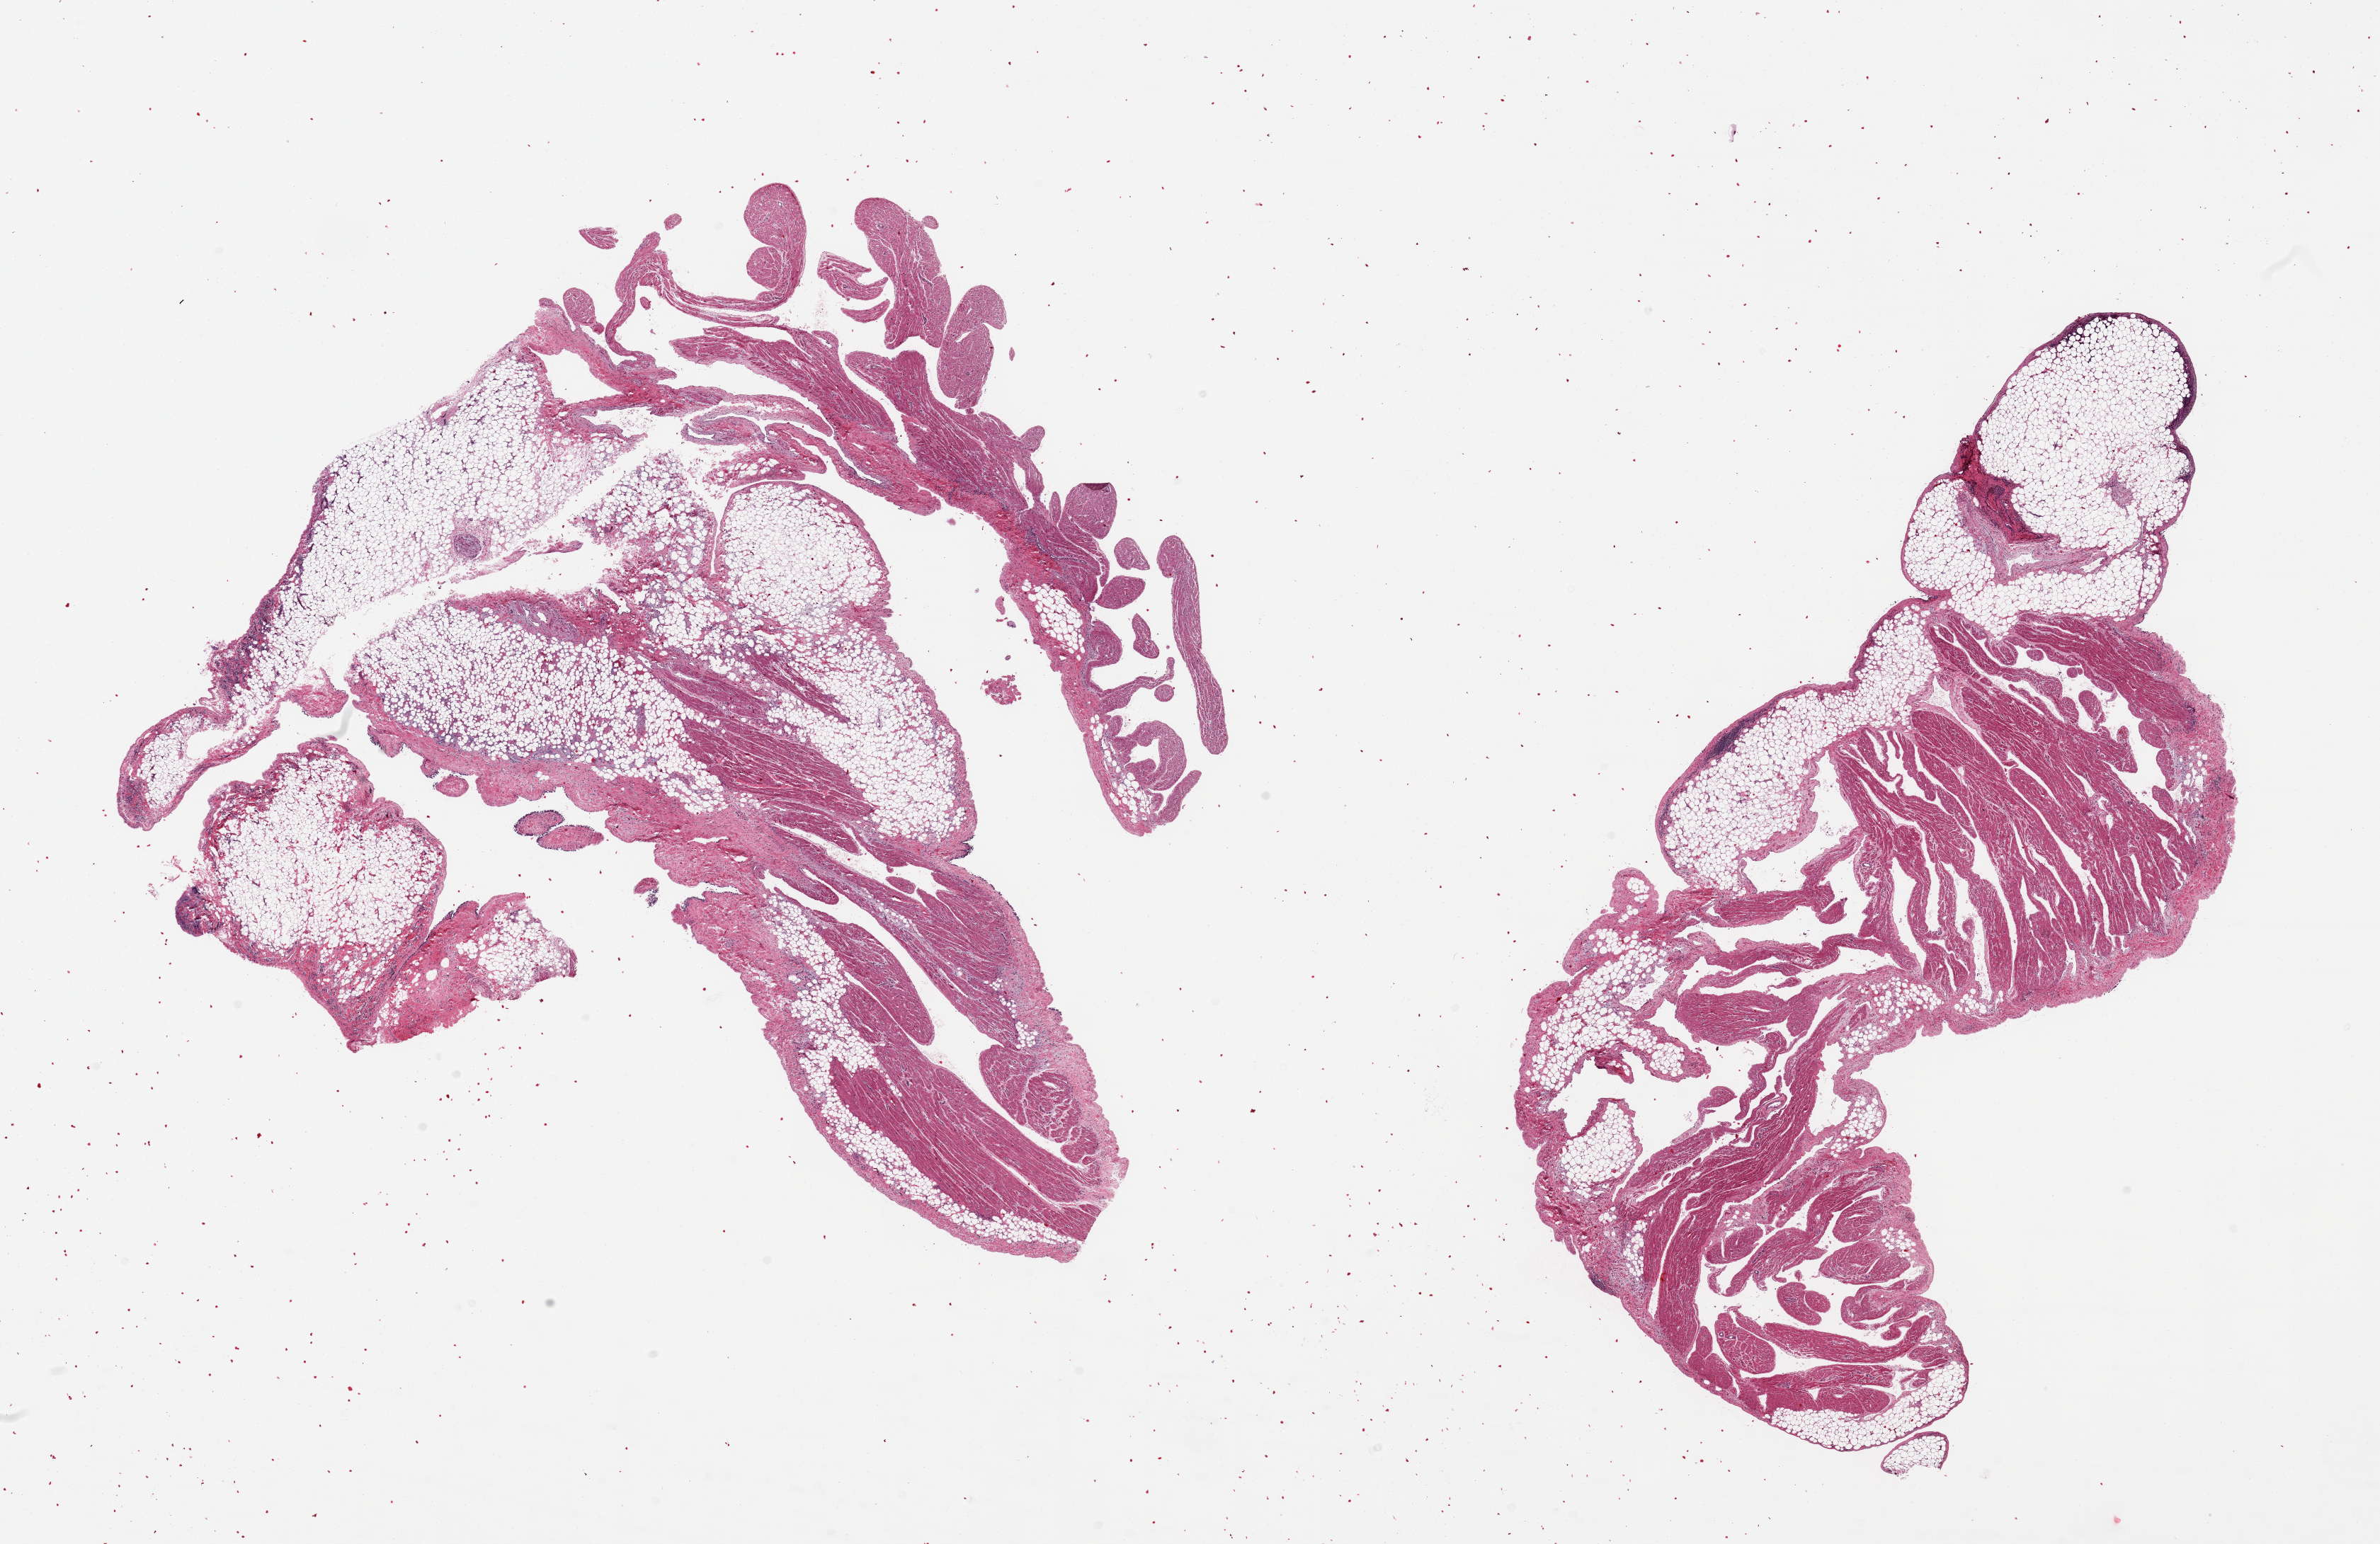
Whole-slide image, haematoxylin and eosin stain — a low-resolution overview of the entire scanned area, about 26.6 x 17.2 mm, PAXgene-fixed, paraffin-embedded tissue, section of auricular appendage (target tissue), donor tissue sample. Donor sex: male.
• review note (as recorded): 2 pieces; from 50-70% fat/fibrous, few collections of predominantly chronic inflammatory cells